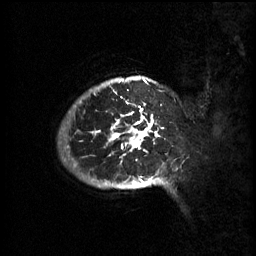
Breast MRI (dynamic contrast-enhanced), one sagittal slice. Slice 53 of 60 in the series (ordered by position). 3 images stored at this slice position (order not interpretable as contrast timing). 1.5 T. TE 4.2 ms, TR 11 ms. 2 mm slice thickness. 256 × 256 image matrix, field of view 220 × 220 mm. Patient: female, 51 years.
Structures marked on this image (semi-automatic segmentation, software-assisted and operator-edited):
- analysis volume of interest (the breast-tissue region the enhancement analysis was run in; not a lesion): bounding box [x1, y1, x2, y2] px = [76, 80, 168, 189]
- tumour enhancement mask (voxels above the 70 % enhancement threshold inside the analysis volume of interest): [92, 80, 162, 187]